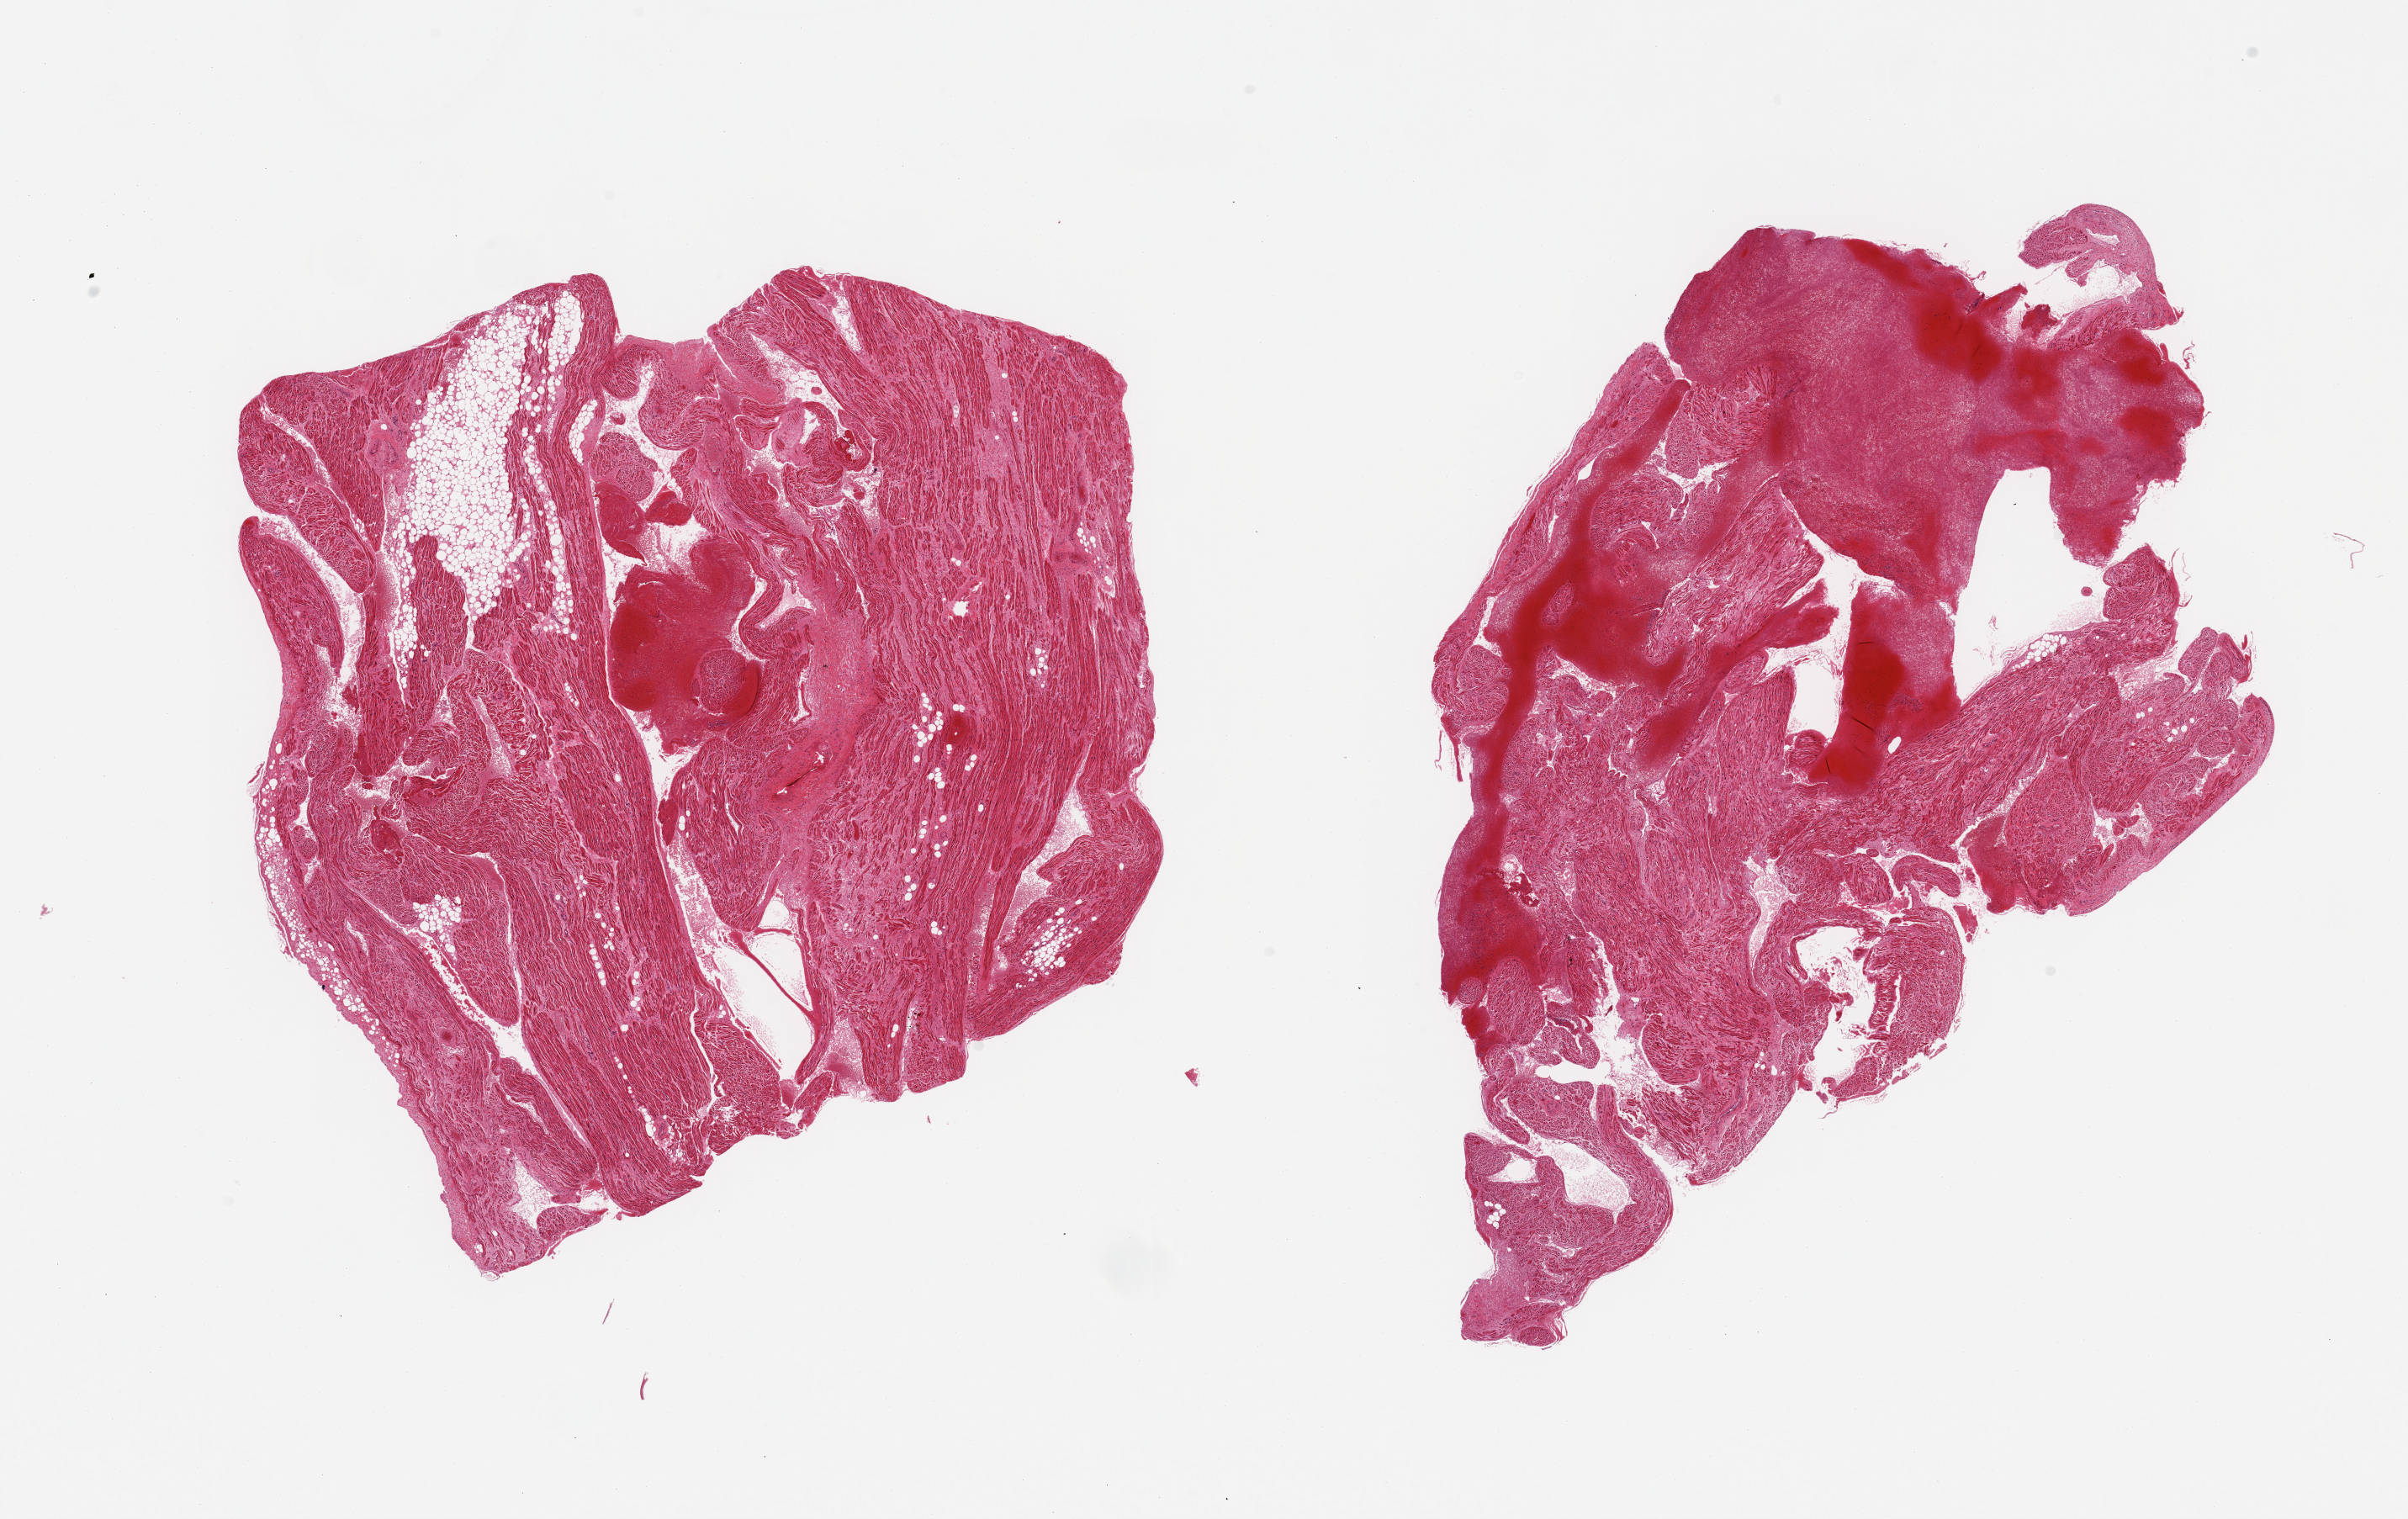
Whole-slide image, haematoxylin and eosin stain — shown as a low-resolution overview of the whole scanned area (about 22.6 x 14.3 mm); PAXgene-fixed, paraffin-embedded tissue; sampled site (target tissue): auricular appendage; donor tissue sample. Donor: female.
Reviewer comment on this tissue sample: 2 pieces; up to 40% blood clots; 10% internal fat.